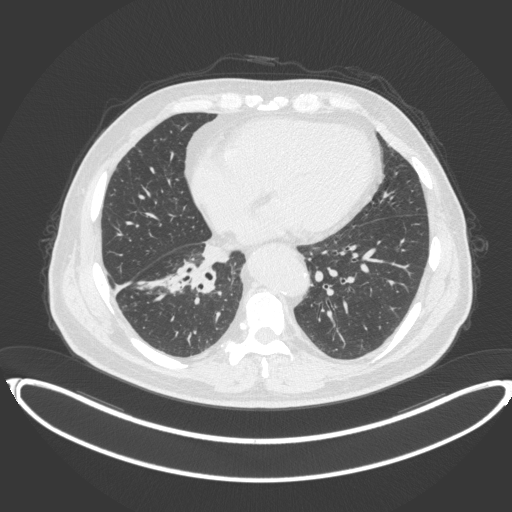
Chest CT, one axial slice. Slice 155 of 383 in the series (ordered by position). Reconstruction kernel B31f. Lung window (W 1500 / L -600 HU). 1 mm slice thickness. 512 × 512 image matrix, field of view 448 × 448 mm. Male patient, age 61 years. From the clinical record (not read from this slice): clinical TNM (as recorded): T1b N1 M0.
Outlined on this slice (bounding box drawn by a radiologist):
- lung tumour (recorded histology: squamous cell carcinoma): box from (x=165, y=260) to (x=219, y=298) px